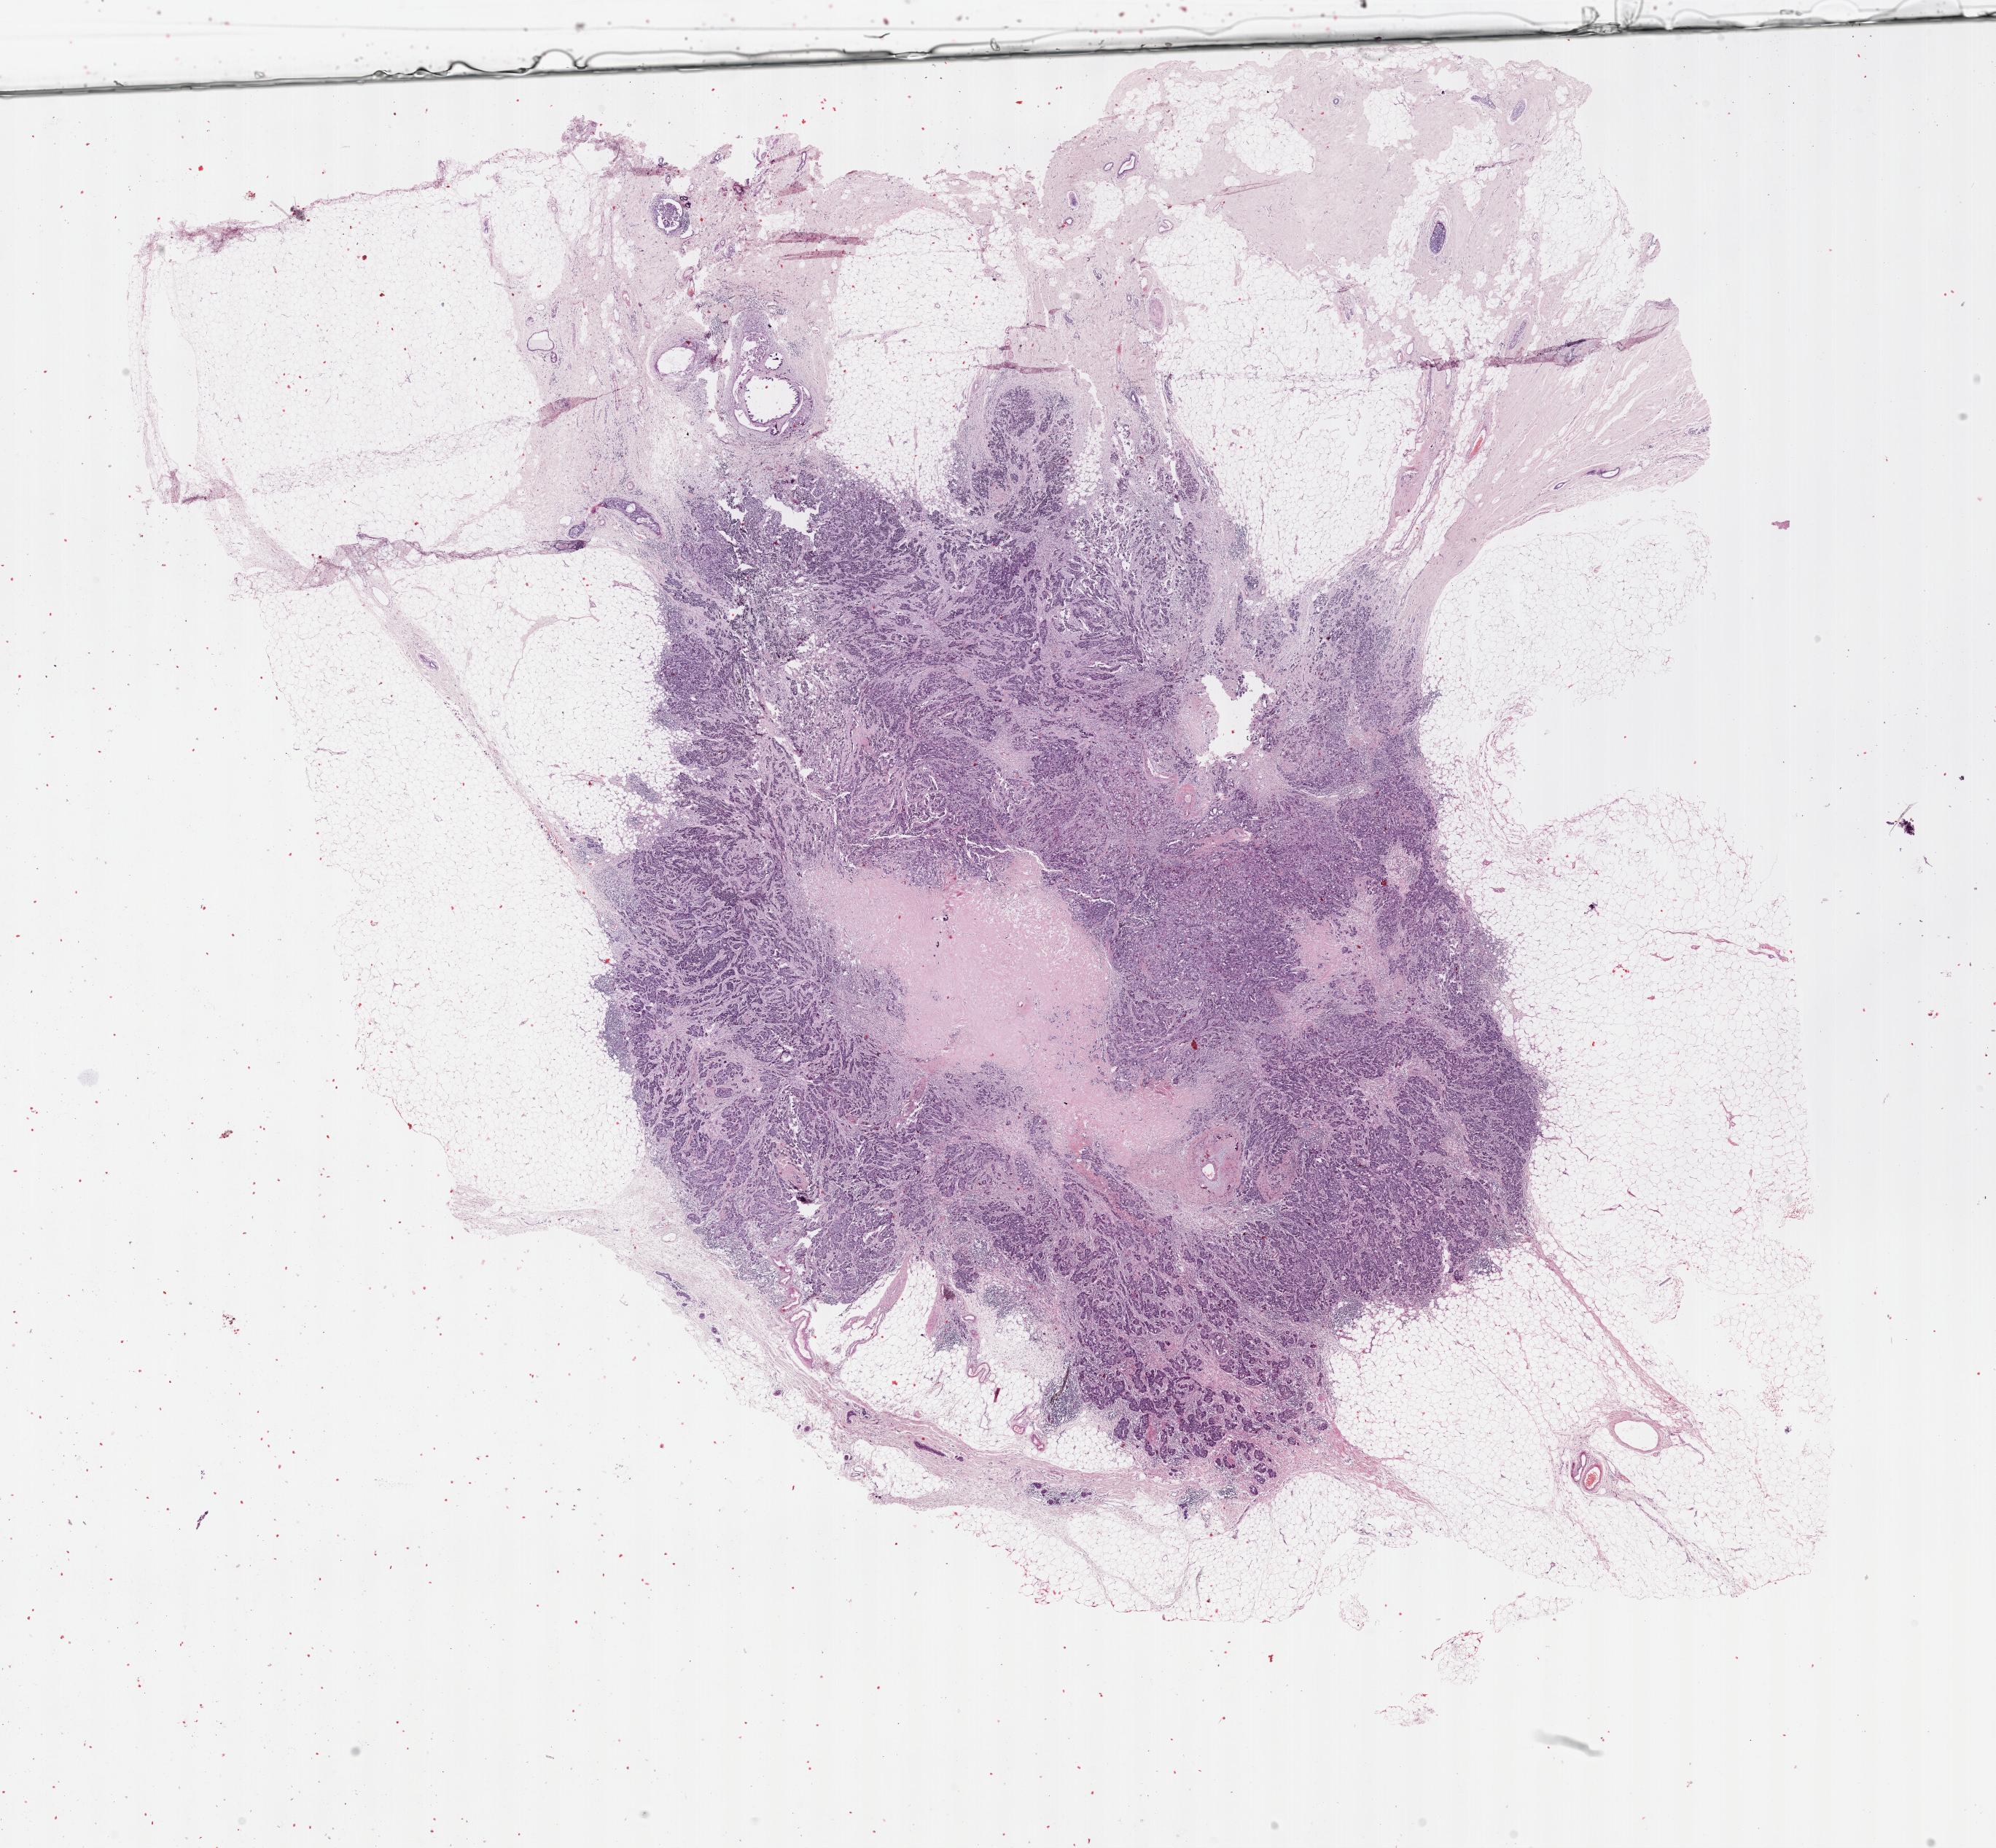
Digitized H&E-stained tissue section (whole slide), low-resolution overview of the scanned area, about 22.1 x 20.5 mm (acquisition: 40x scan); formalin-fixed paraffin-embedded (FFPE) diagnostic section; sample: primary tumour, breast. Female patient; age at initial diagnosis 81 years.
Lymph nodes positive (case pathology): 6 of 14 examined. Pathologic diagnosis: Infiltrating duct carcinoma, NOS. AJCC pathologic stage: IIIA. Laterality: right.